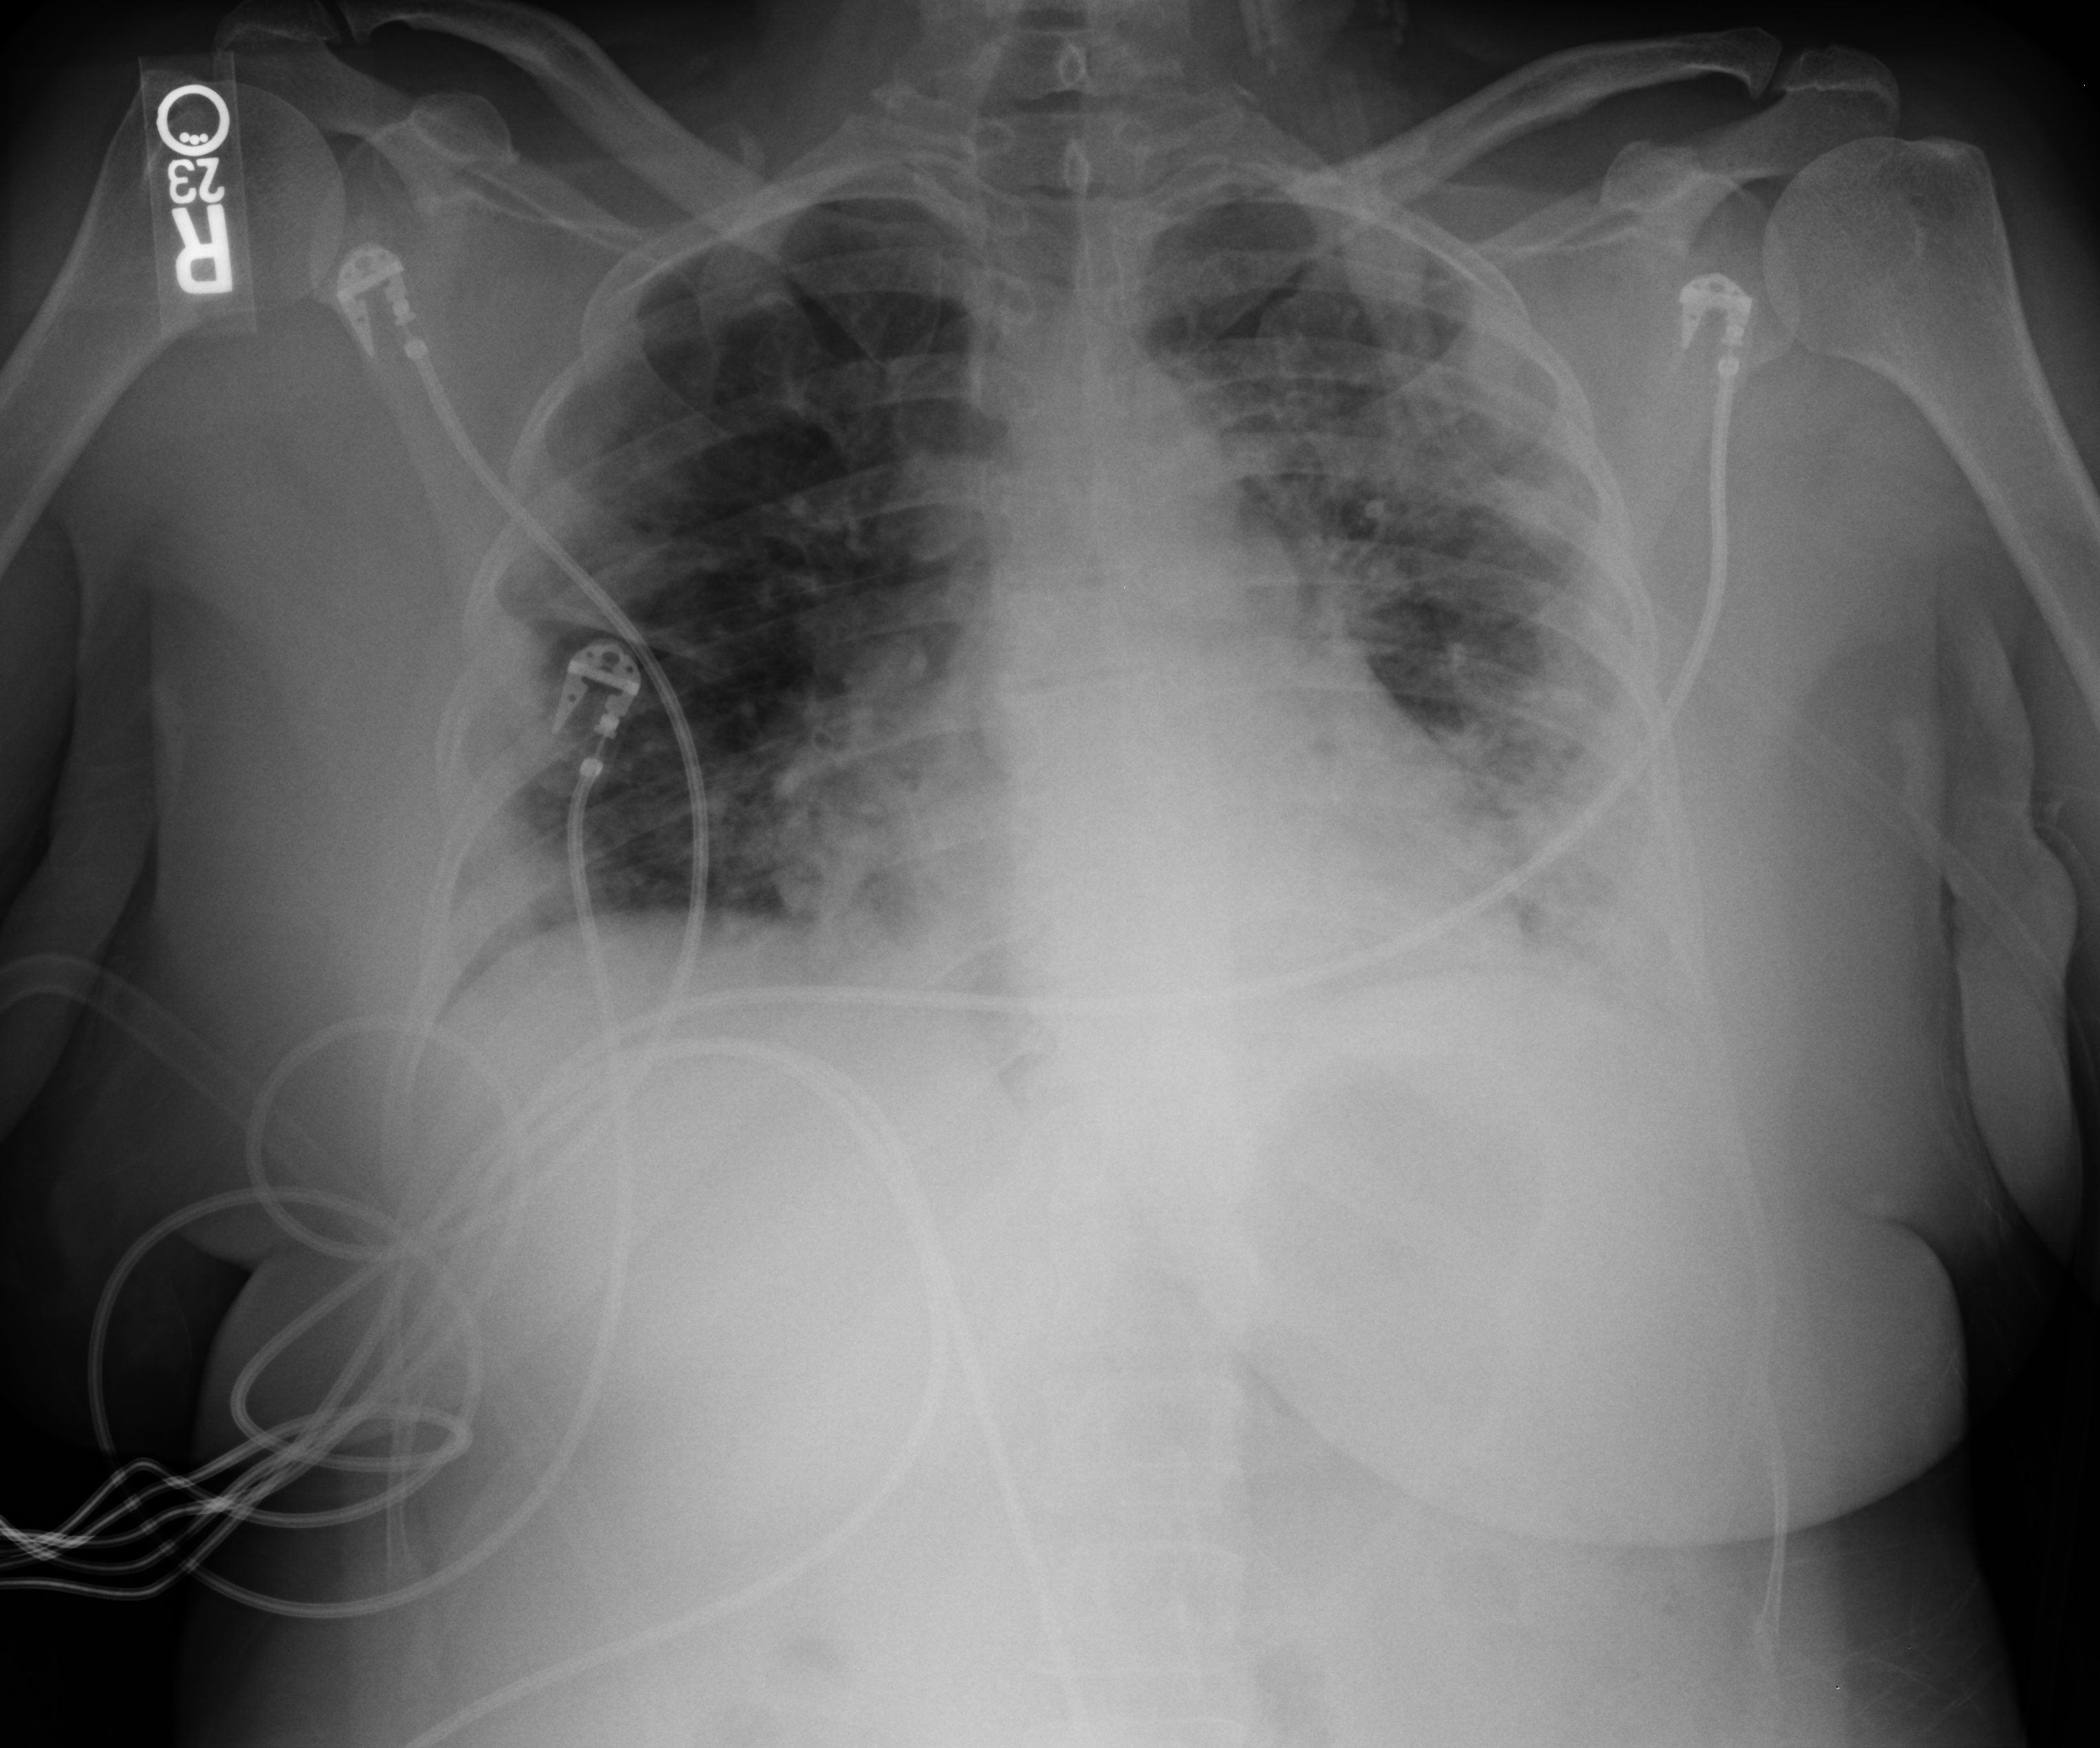
Portable chest radiograph, anteroposterior (AP) projection. Patient hospitalised with COVID-19; female, aged 18–59 years.
From the hospital-stay record, not from the radiograph (when in the stay this image was taken is not recorded): length of hospital stay: 14 days.